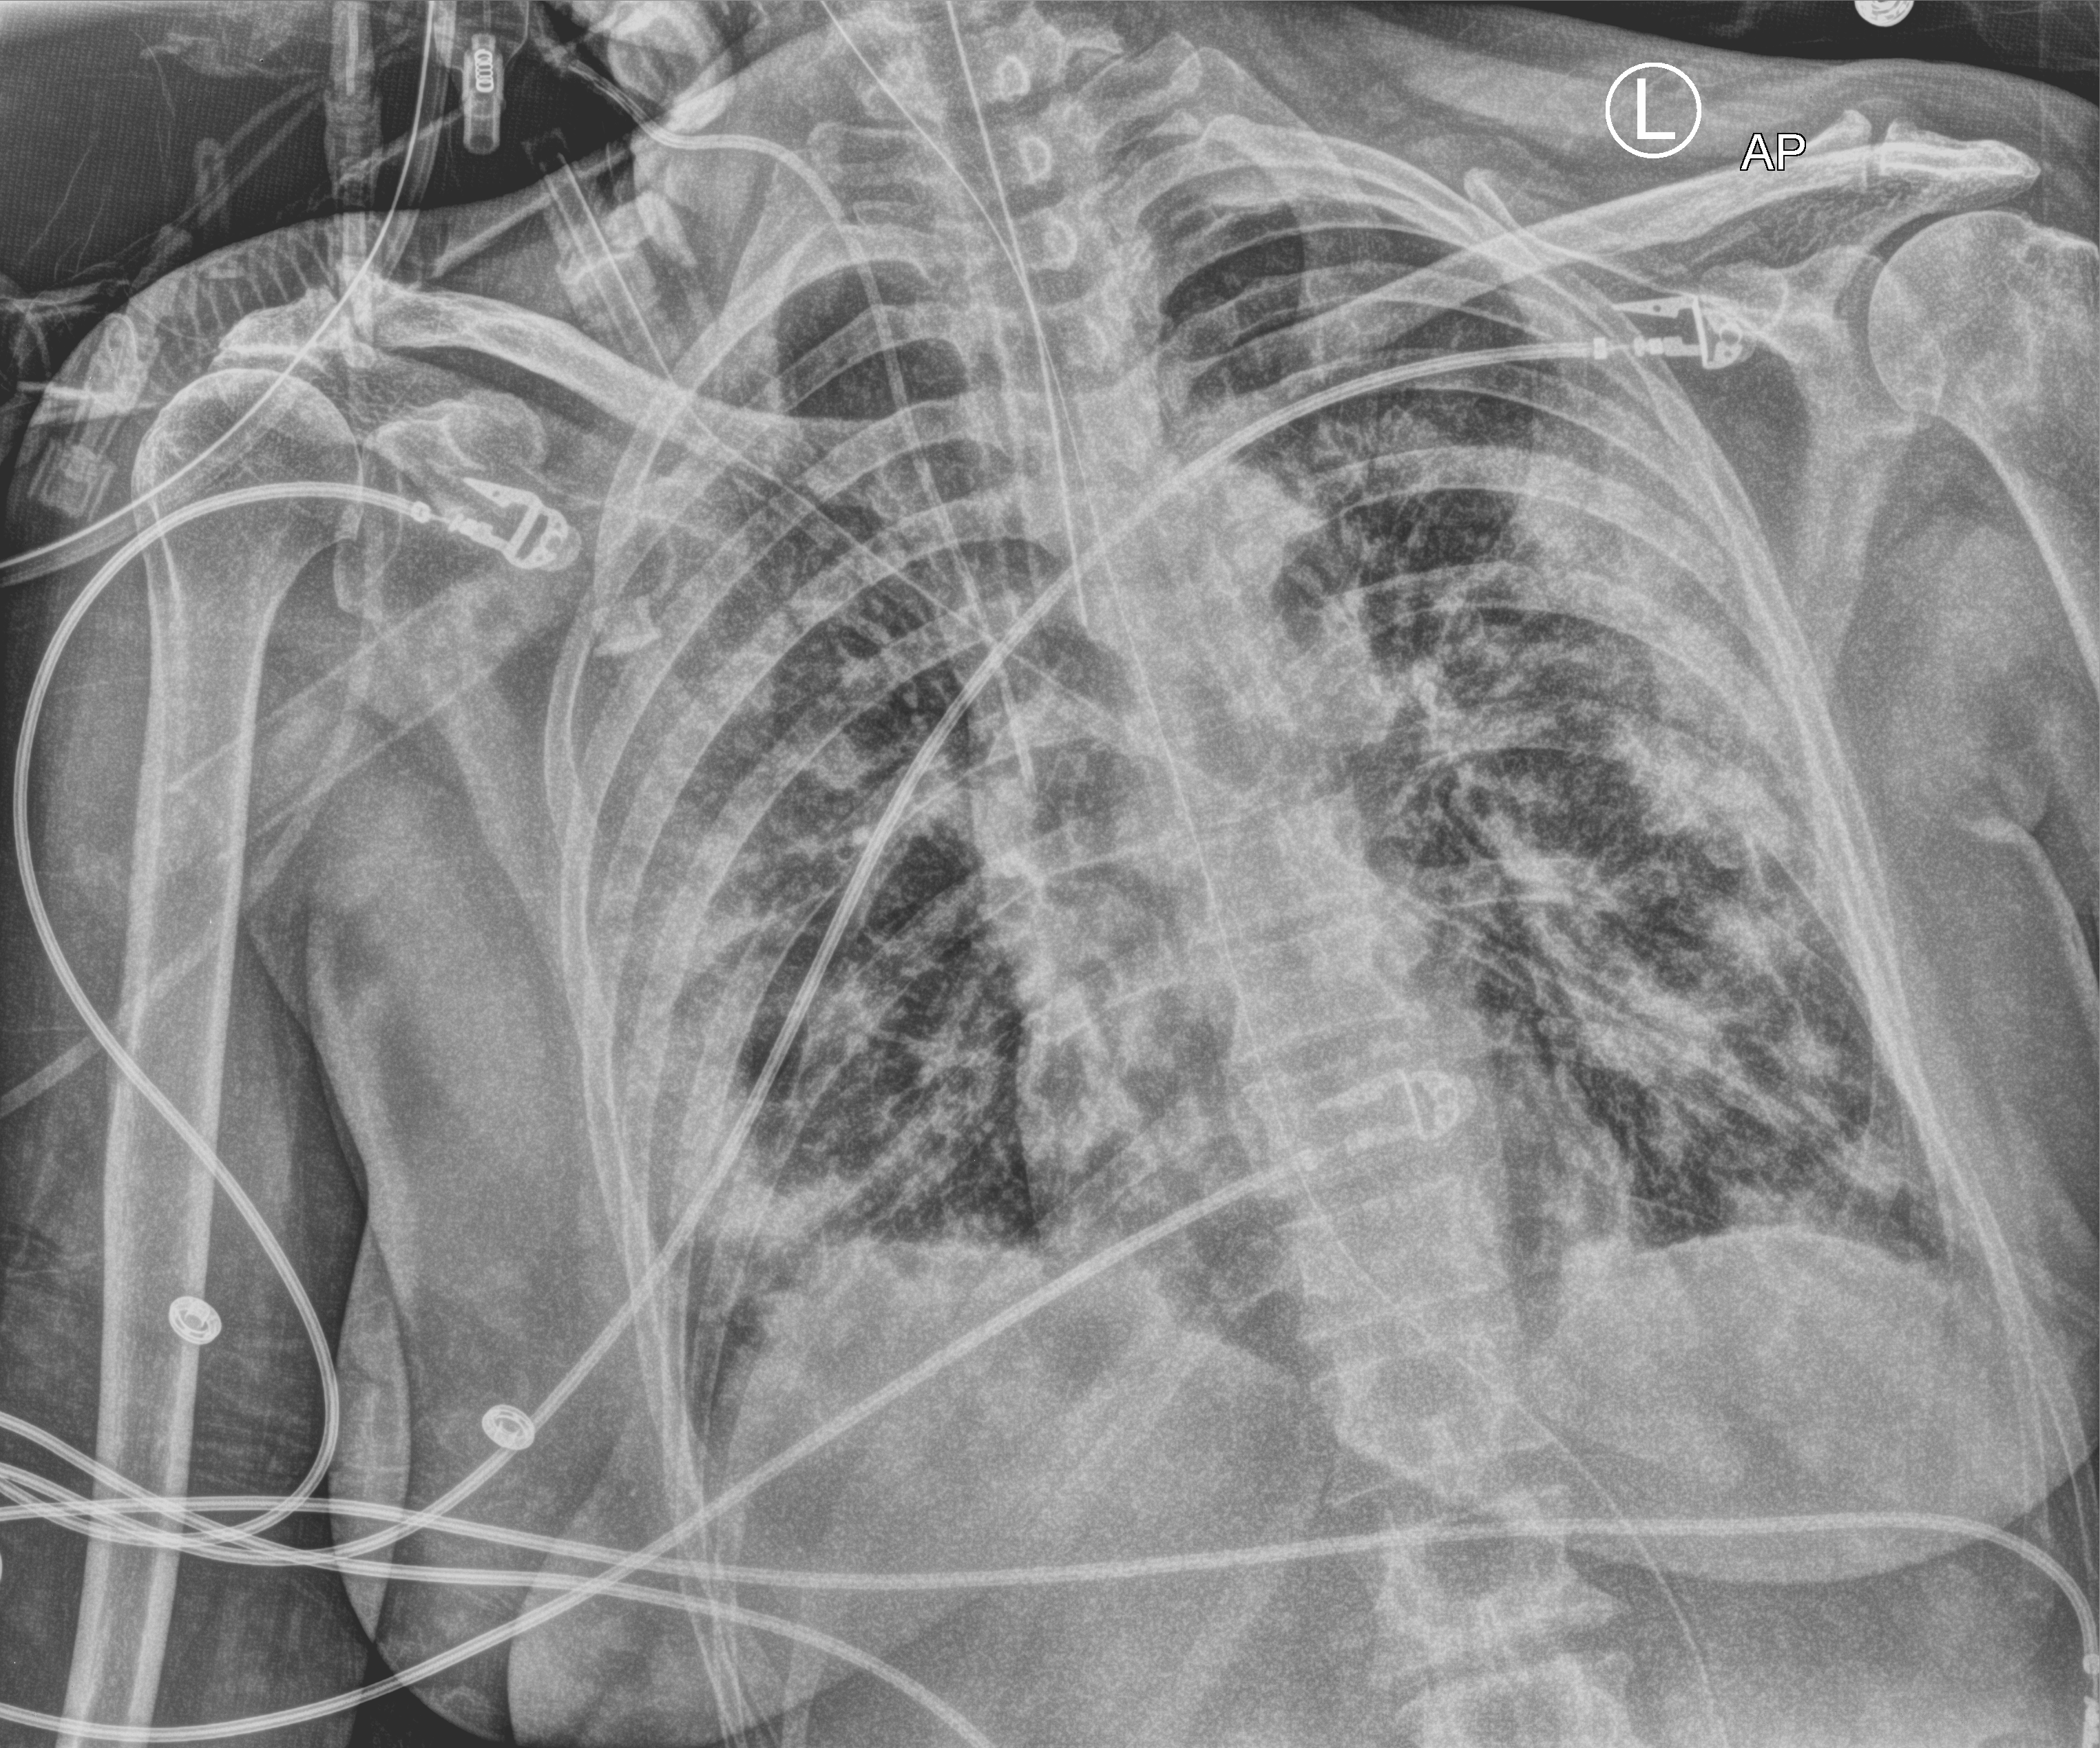
Portable chest radiograph; anteroposterior (AP) projection. Patient hospitalised with COVID-19; female, aged 60–74 years.
Admission-level facts for this patient (not findings on this image; timing relative to this image not recorded):
- mechanically ventilated during this hospital stay: yes
- admitted to intensive care during this hospital stay: yes